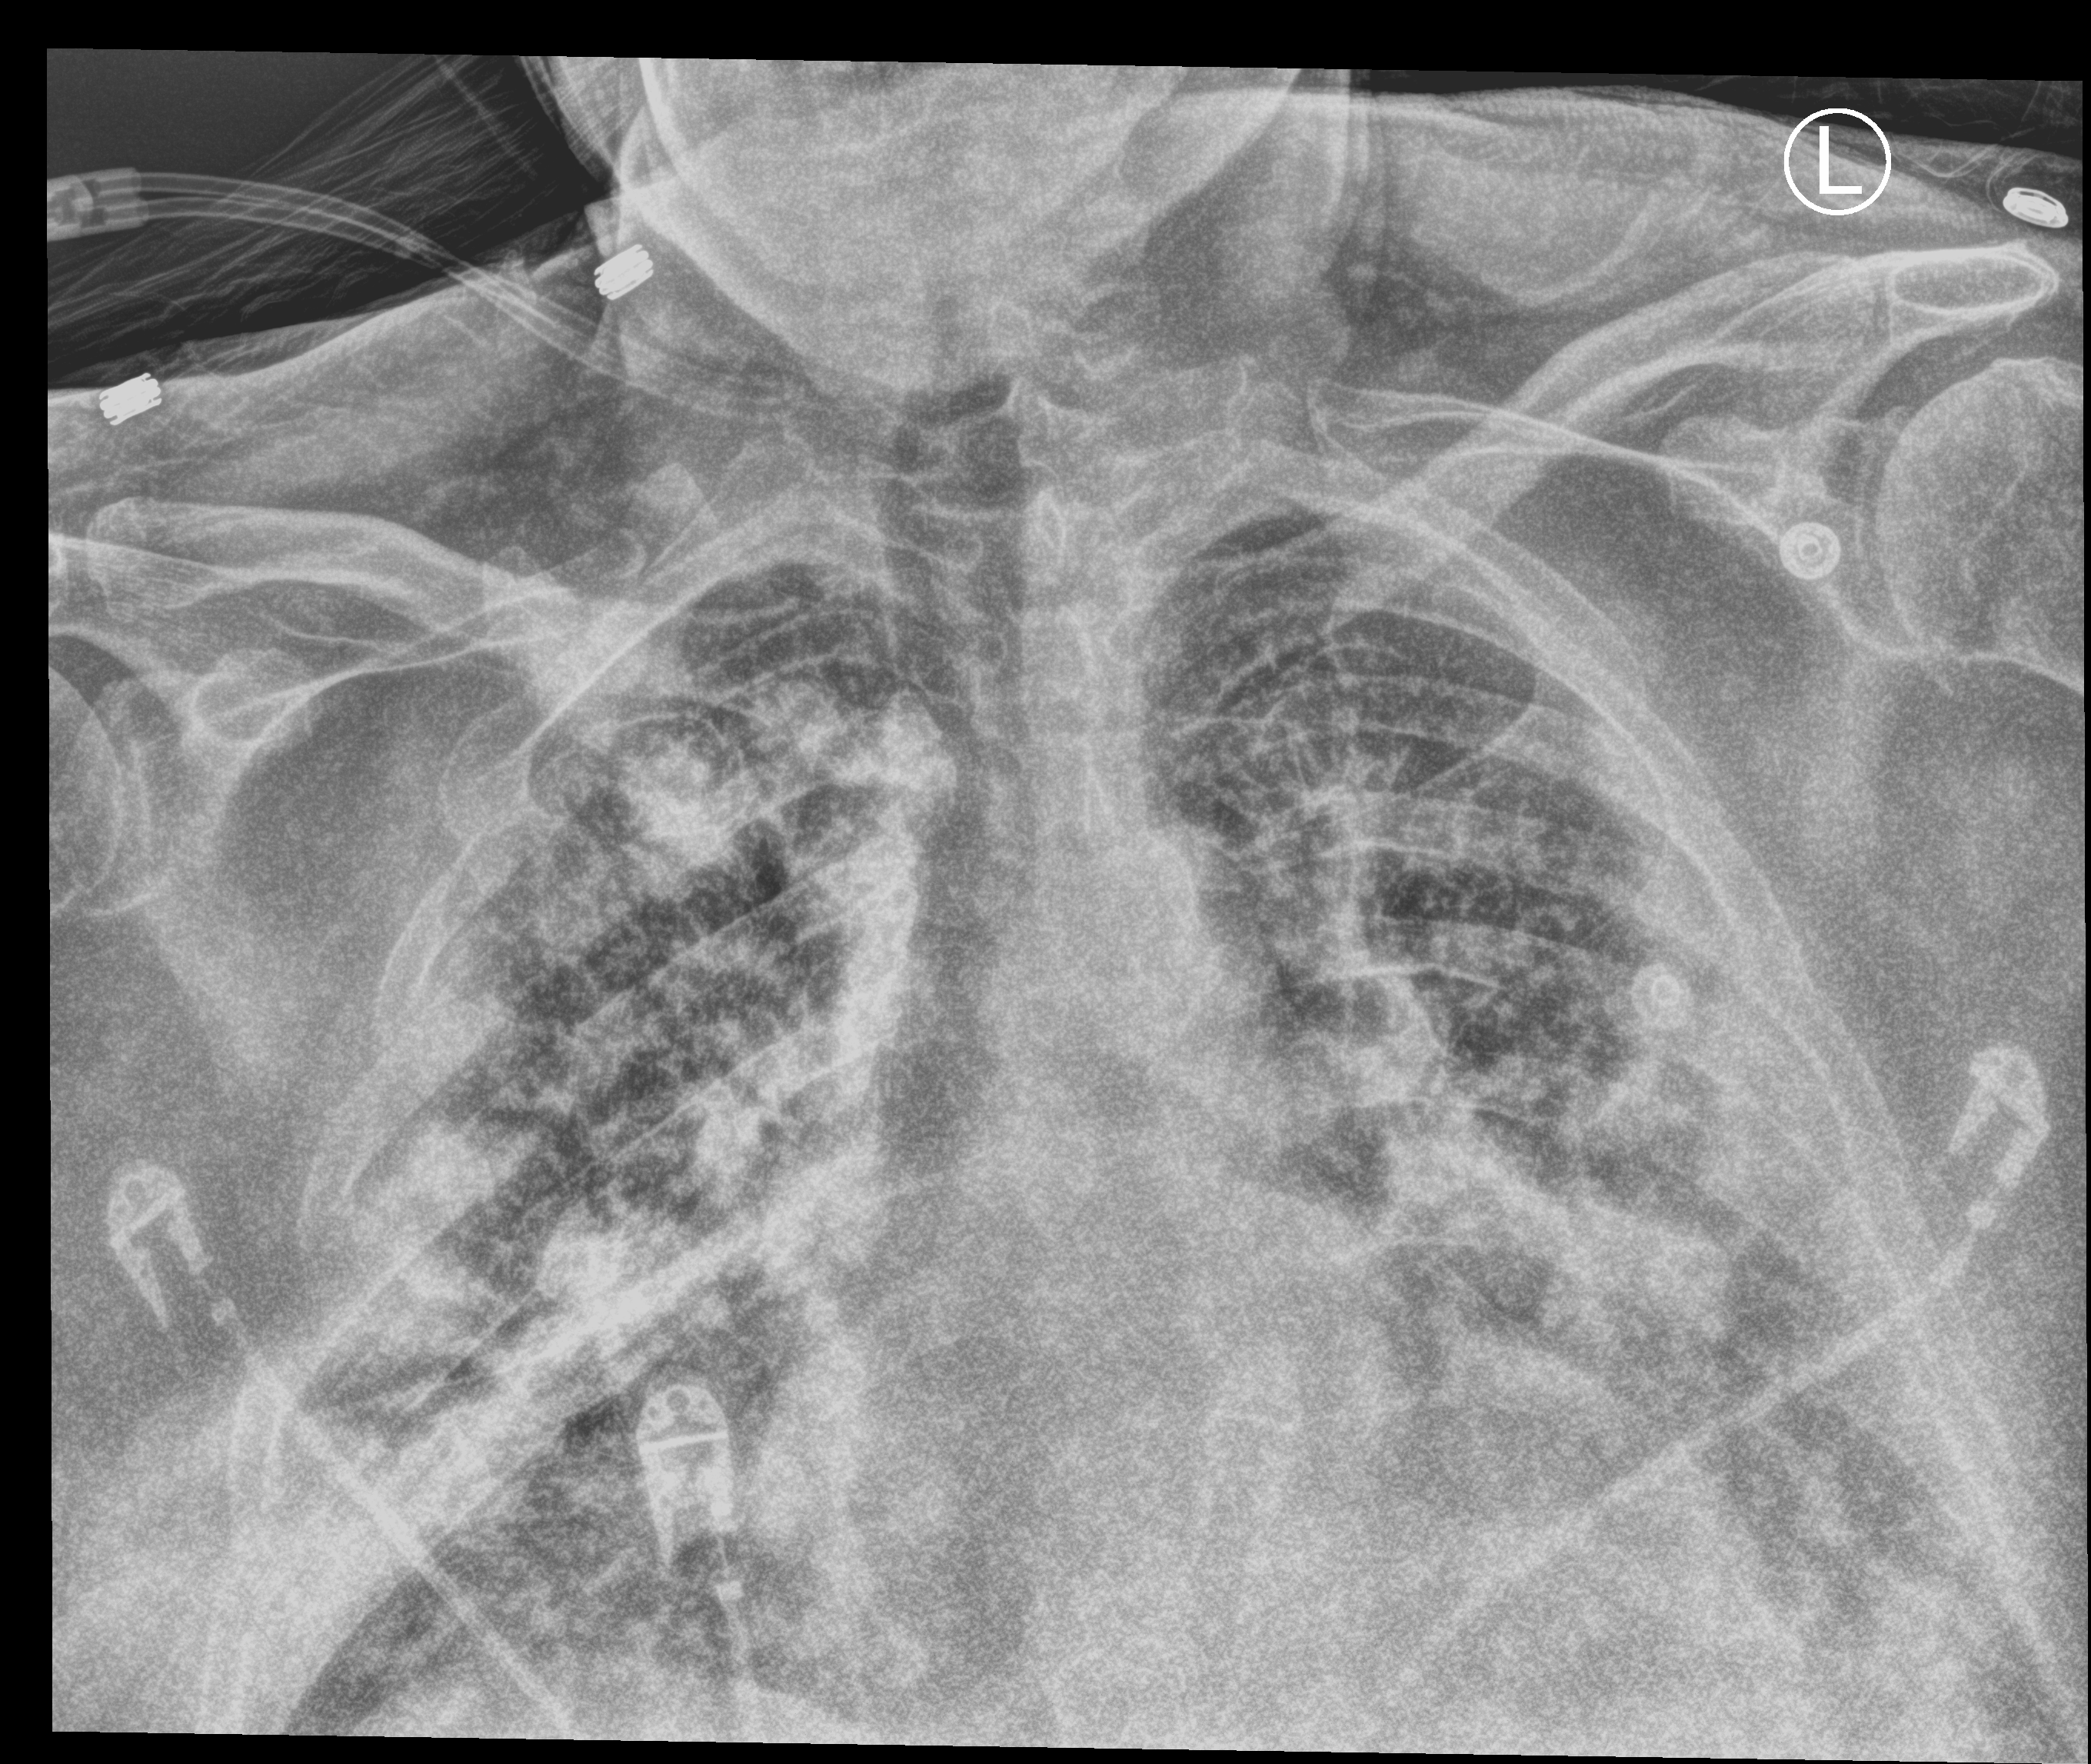
Bedside chest radiograph (computed radiography), anteroposterior (AP) projection. Male patient hospitalised with COVID-19, age 60–74 years.
From the hospital-stay record, not from the radiograph (when in the stay this image was taken is not recorded): admitted to intensive care during this hospital stay: yes; mechanically ventilated during this hospital stay: yes.